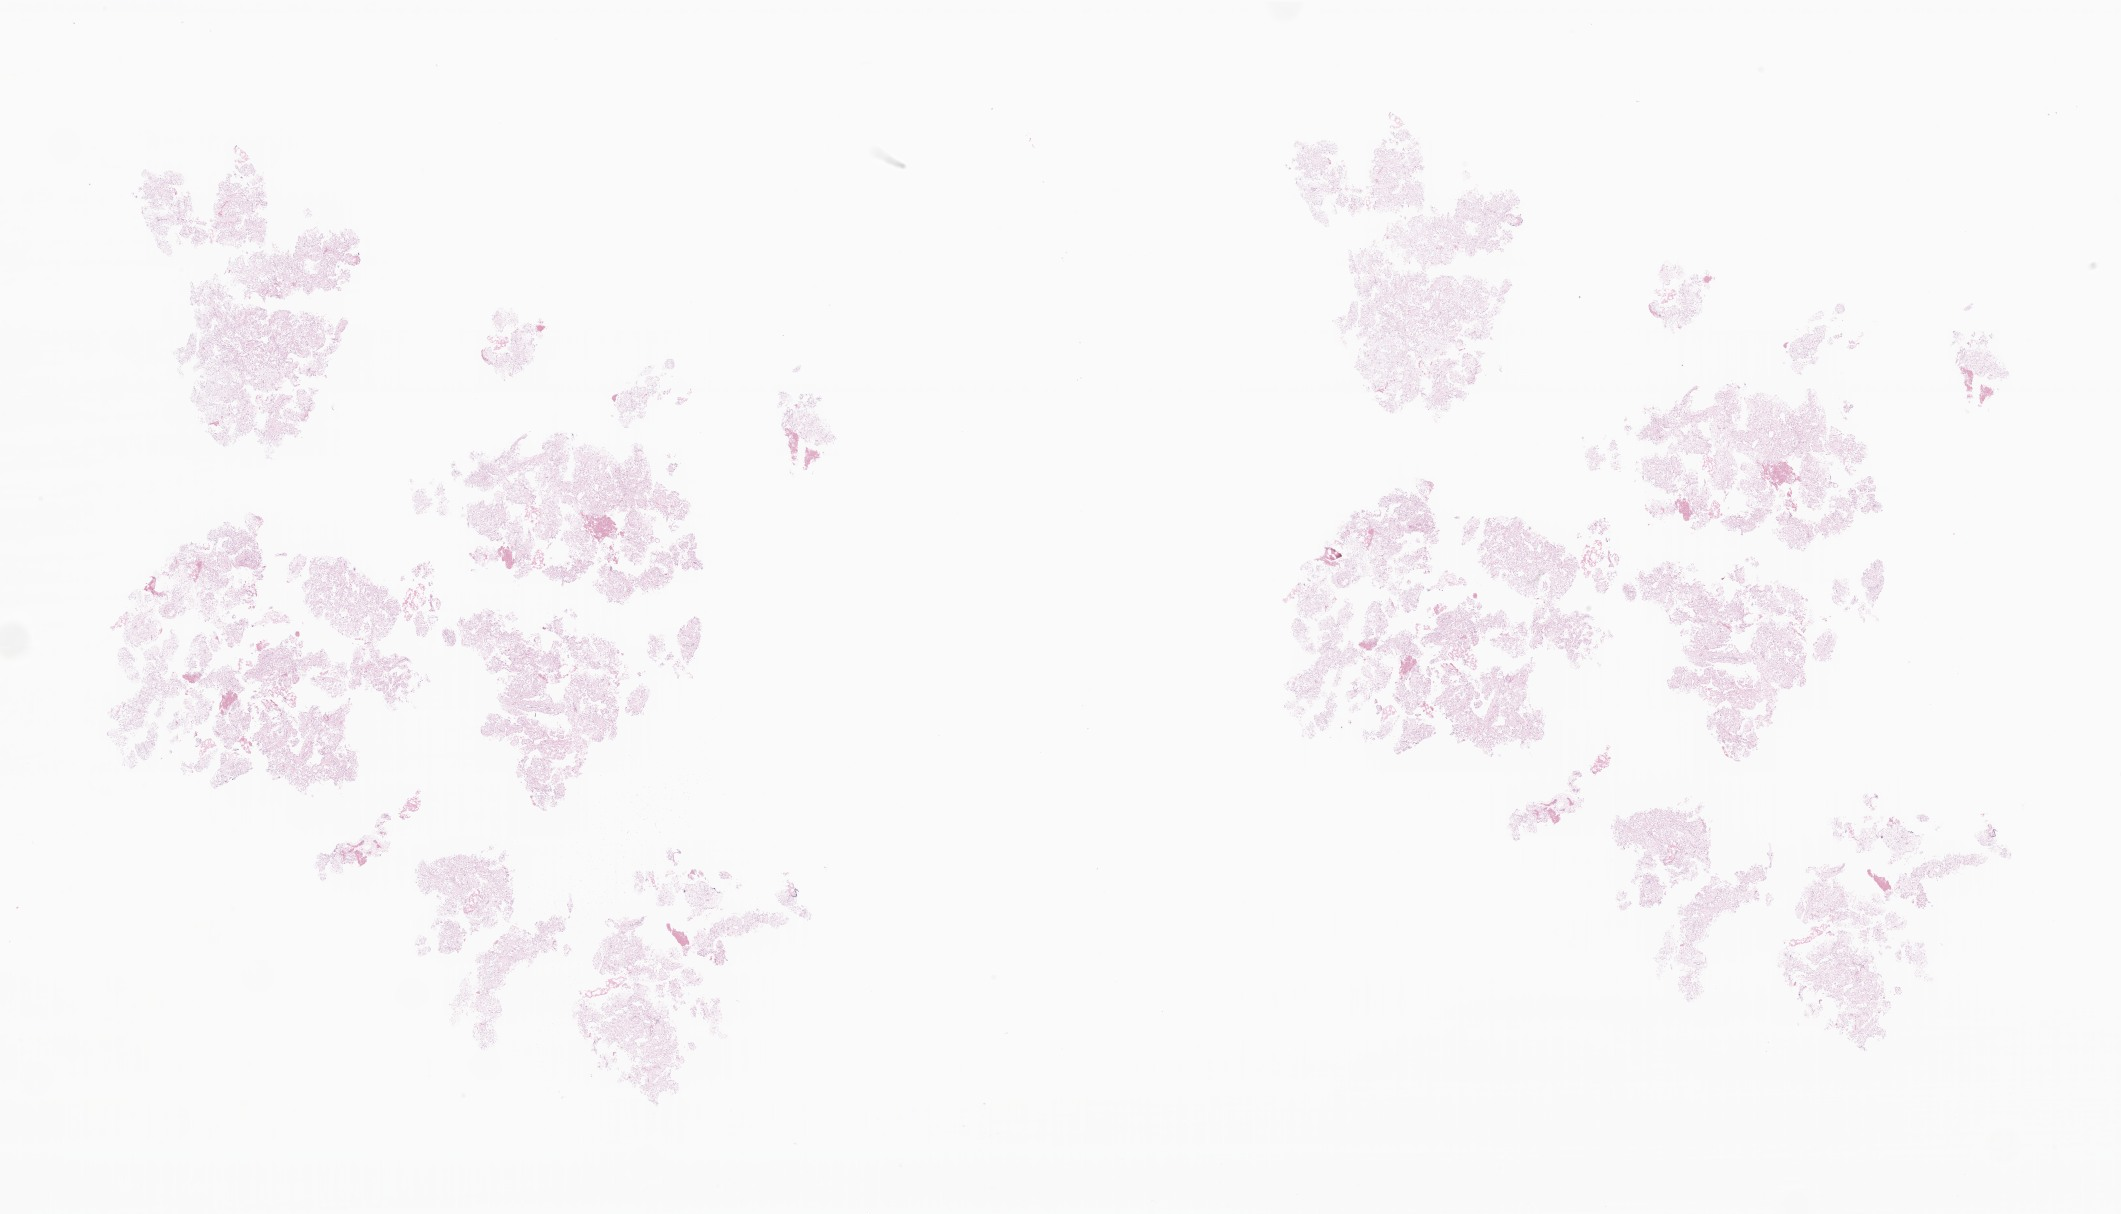
Whole-slide image, hematoxylin and eosin (H&E) stain of tumor tissue from the optic nerve, a low-resolution overview of the entire scanned area, about 35.8 x 20.5 mm; formalin-fixed, paraffin-embedded (FFPE) tissue. Female patient, age 178 months.
Diagnosis: Pilocytic astrocytoma.